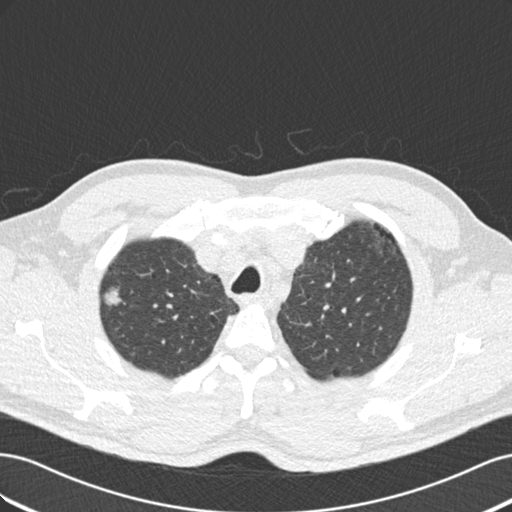
Low-dose screening chest CT, one axial slice. Reconstruction kernel B30f. Lung window (W 1500 / L -600 HU). 2 mm slice thickness. 512 × 512 image matrix, field of view 360 × 360 mm.
Structures marked on this image (expert manual segmentation):
- lesion 1 (tumor, upper lobe of right lung): bounding box (x1, y1, x2, y2) in pixels: (104, 287, 122, 306)